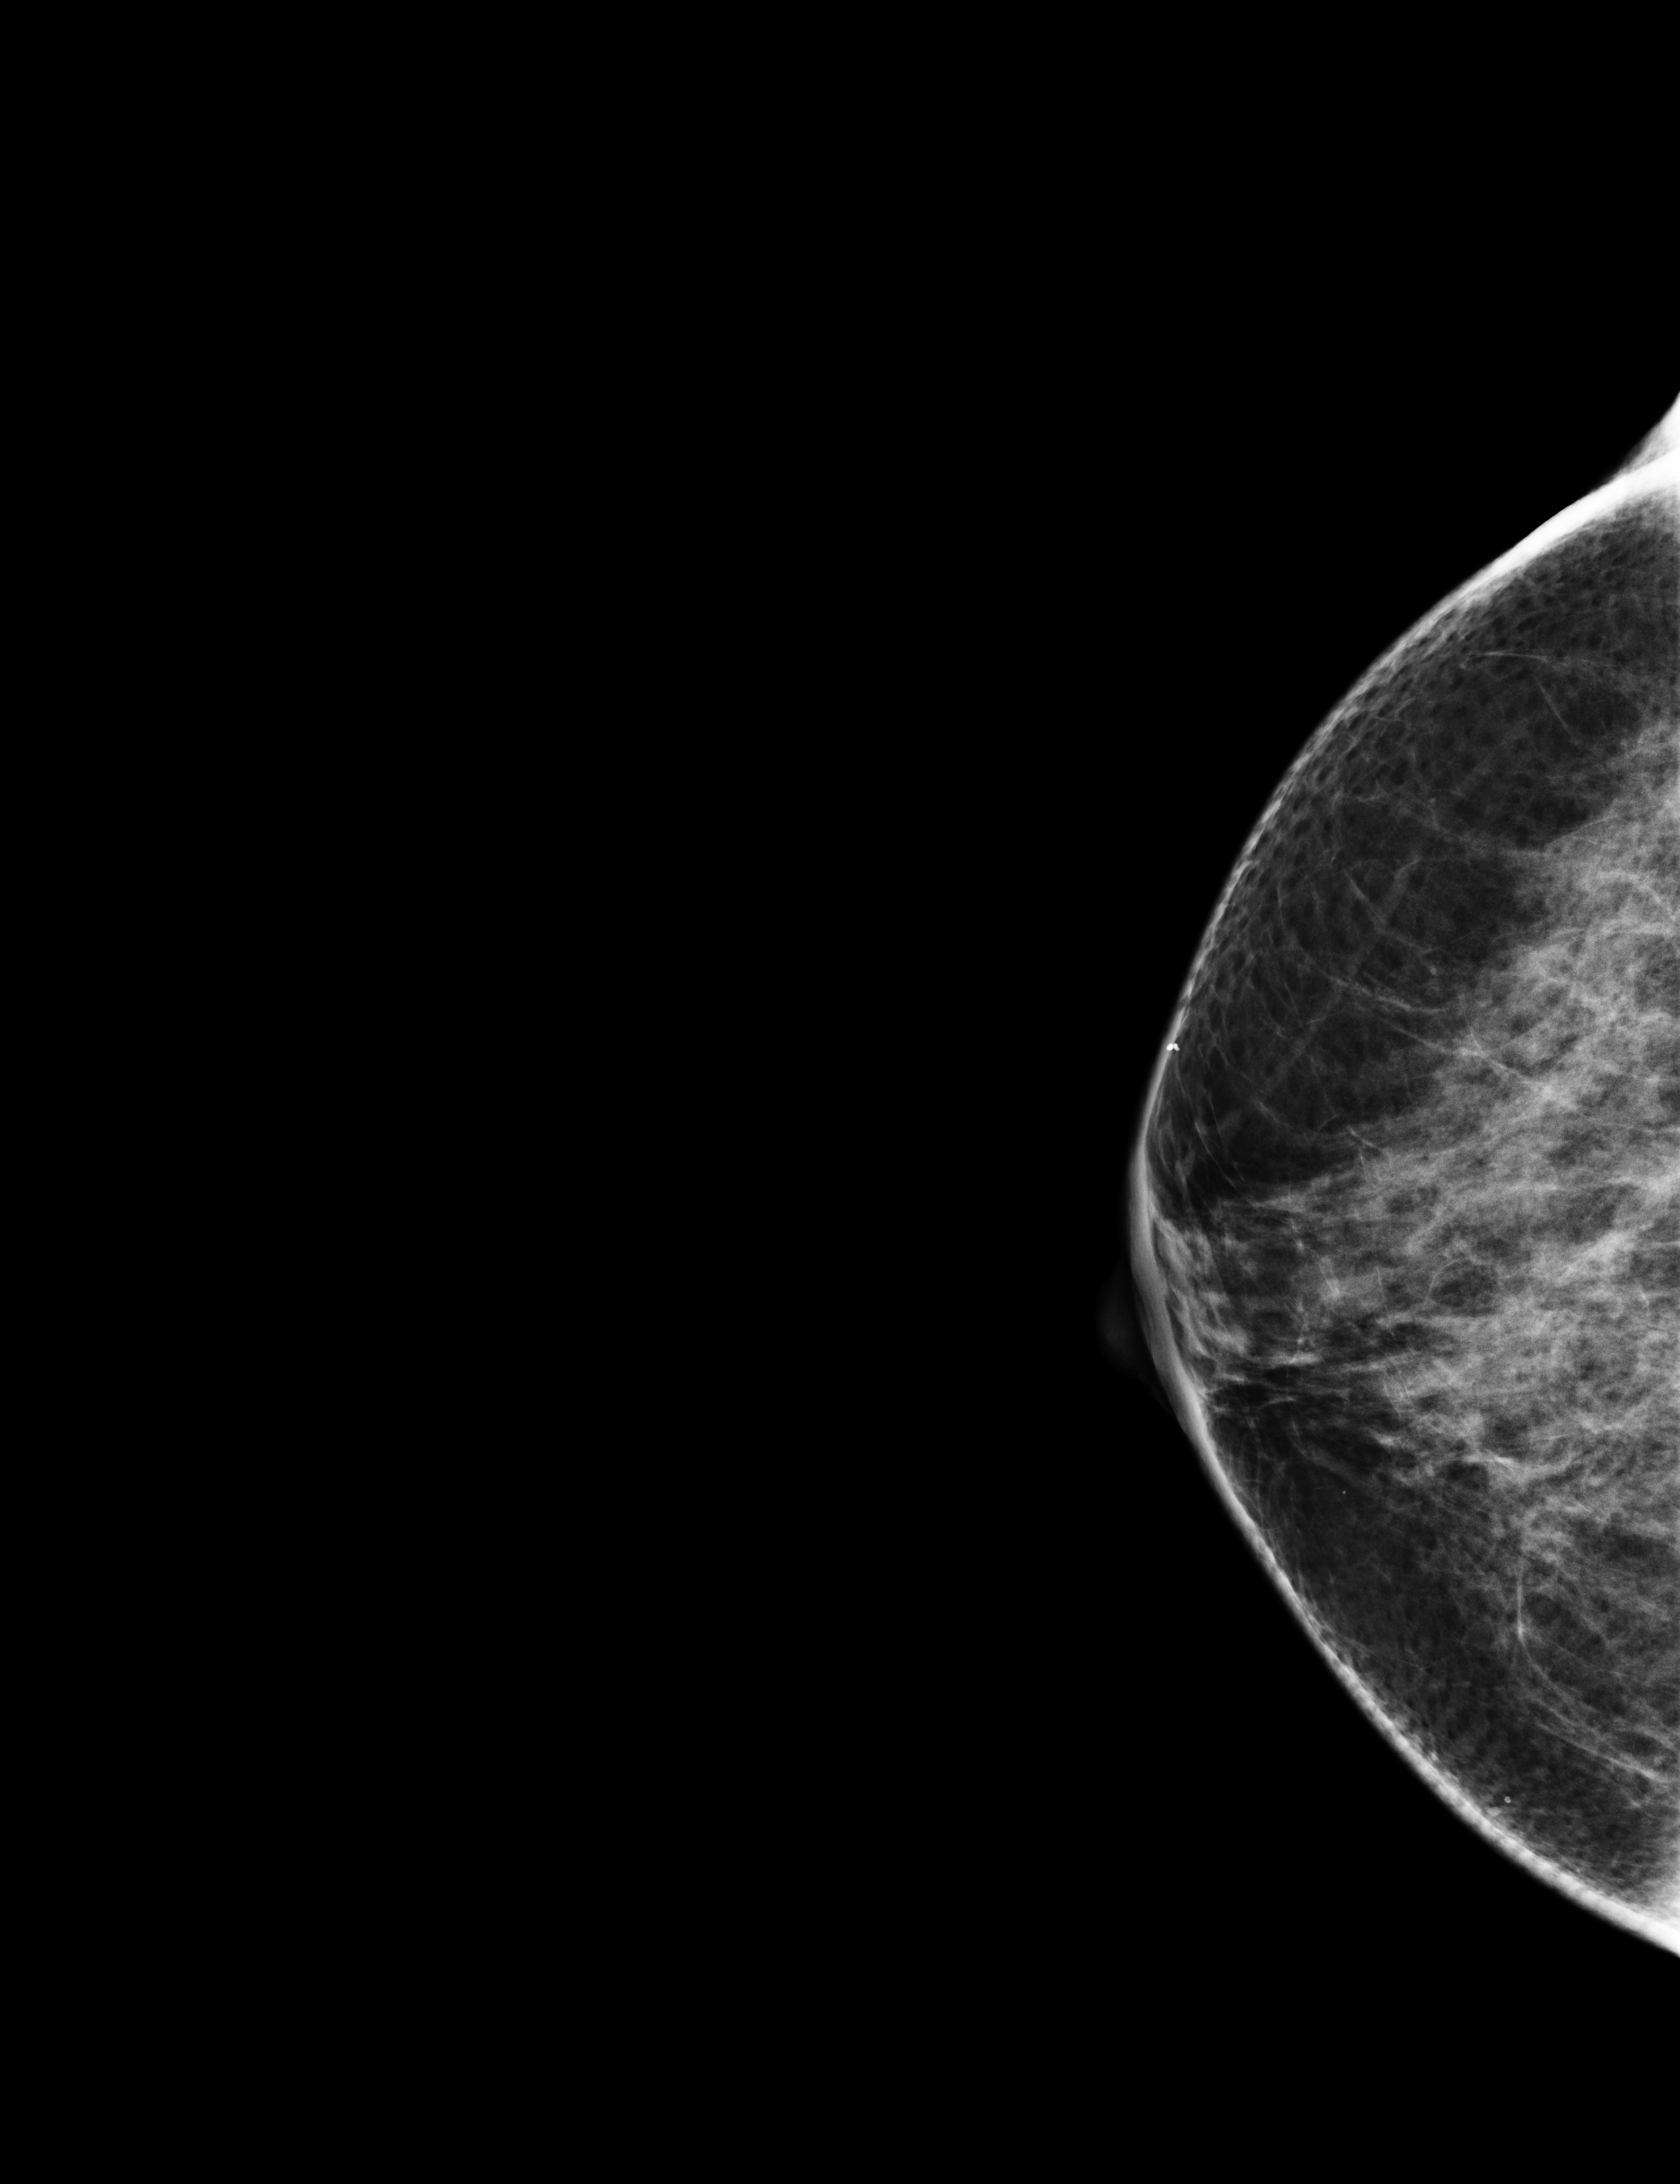
Screening examination, compressed breast thickness 63 mm. Female patient, age 43 years.
Image type: full-field digital mammogram. Breast: right. Projection: cranio-caudal projection.